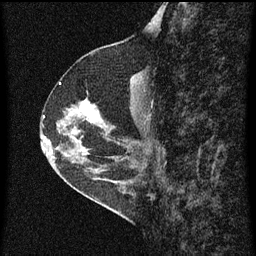
Breast MRI (dynamic contrast-enhanced), one sagittal slice. Position 28 of 60 along the scan axis. Dynamic contrast-enhanced series, image 2 of 3 at this slice position (ordered by acquisition). 1.5 T. TE 4.2 ms, TR 8 ms. 2 mm slice thickness. 256 × 256 image matrix, field of view 180 × 180 mm. Female patient, age 56 years.
Structures marked on this image (semi-automatically segmented with operator editing):
- analysis volume of interest (the breast-tissue region the enhancement analysis was run in; not a lesion): box from (x=49, y=96) to (x=110, y=159) px
- tumour enhancement mask (voxels above the 70 % enhancement threshold inside the analysis volume of interest): (x=80, y=102)–(x=99, y=123)